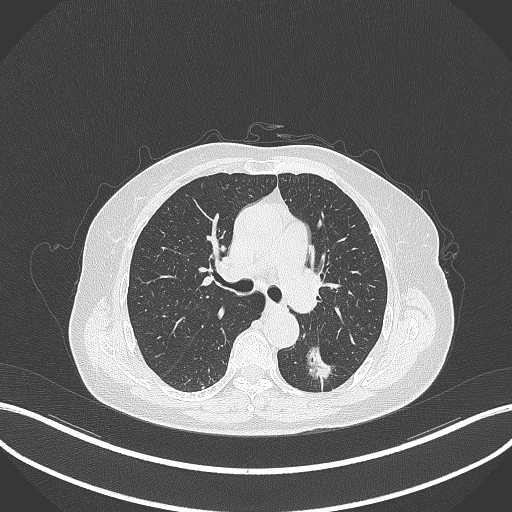
Chest CT, one axial slice. 120 kVp. Lung window (W 1500 / L -600 HU). 1 mm slice thickness. 512 × 512 image matrix, field of view 400 × 400 mm. Patient: female, 70 years. Case-level facts recorded for this patient, not image findings: clinical TNM (as recorded): T1c N0 M0.
Structures marked on this image (rectangle marked by the reading radiologist):
- lung tumour (recorded histology: adenocarcinoma): bounding box [x1, y1, x2, y2] px = [300, 337, 337, 383]